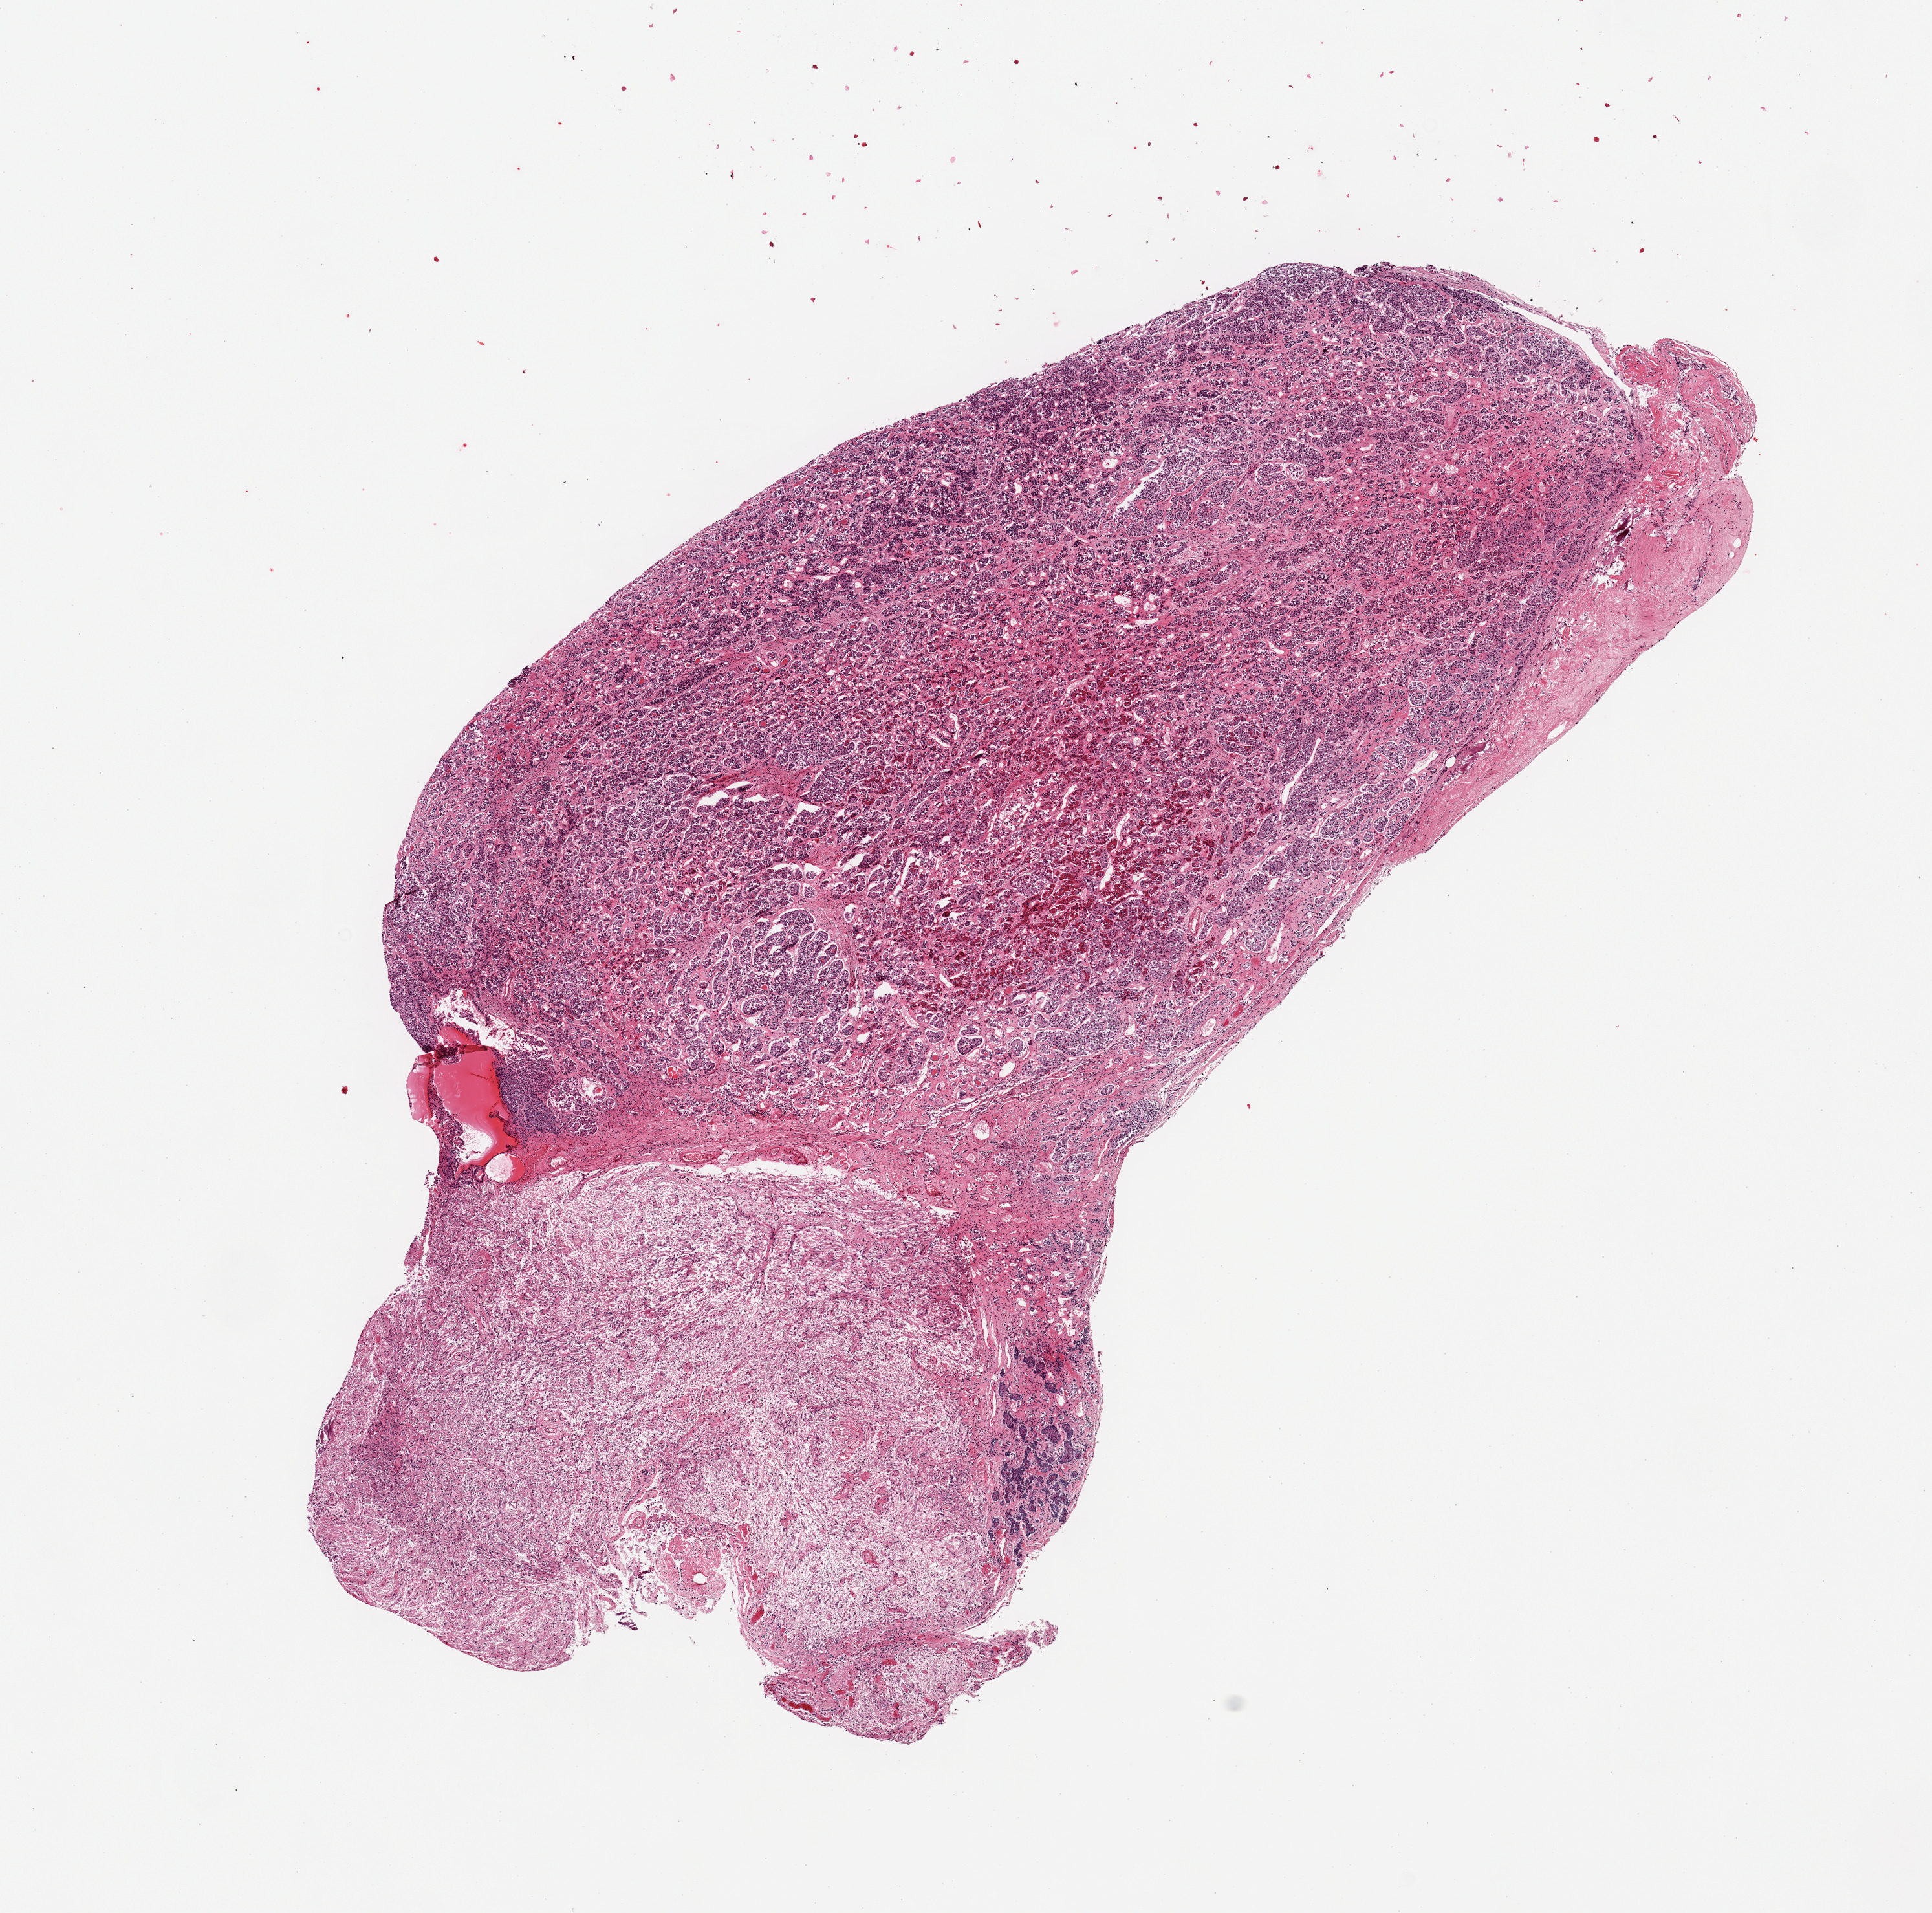
Whole-slide image, hematoxylin and eosin (H&E) stain, brightfield, whole scanned area (about 11.8 x 11.7 mm) shown as a low-resolution overview. PAXgene-fixed, paraffin-embedded tissue. Section of pituitary (target tissue). Donor tissue sample.
- review note (as recorded): 1 piece; anterior & posterior present